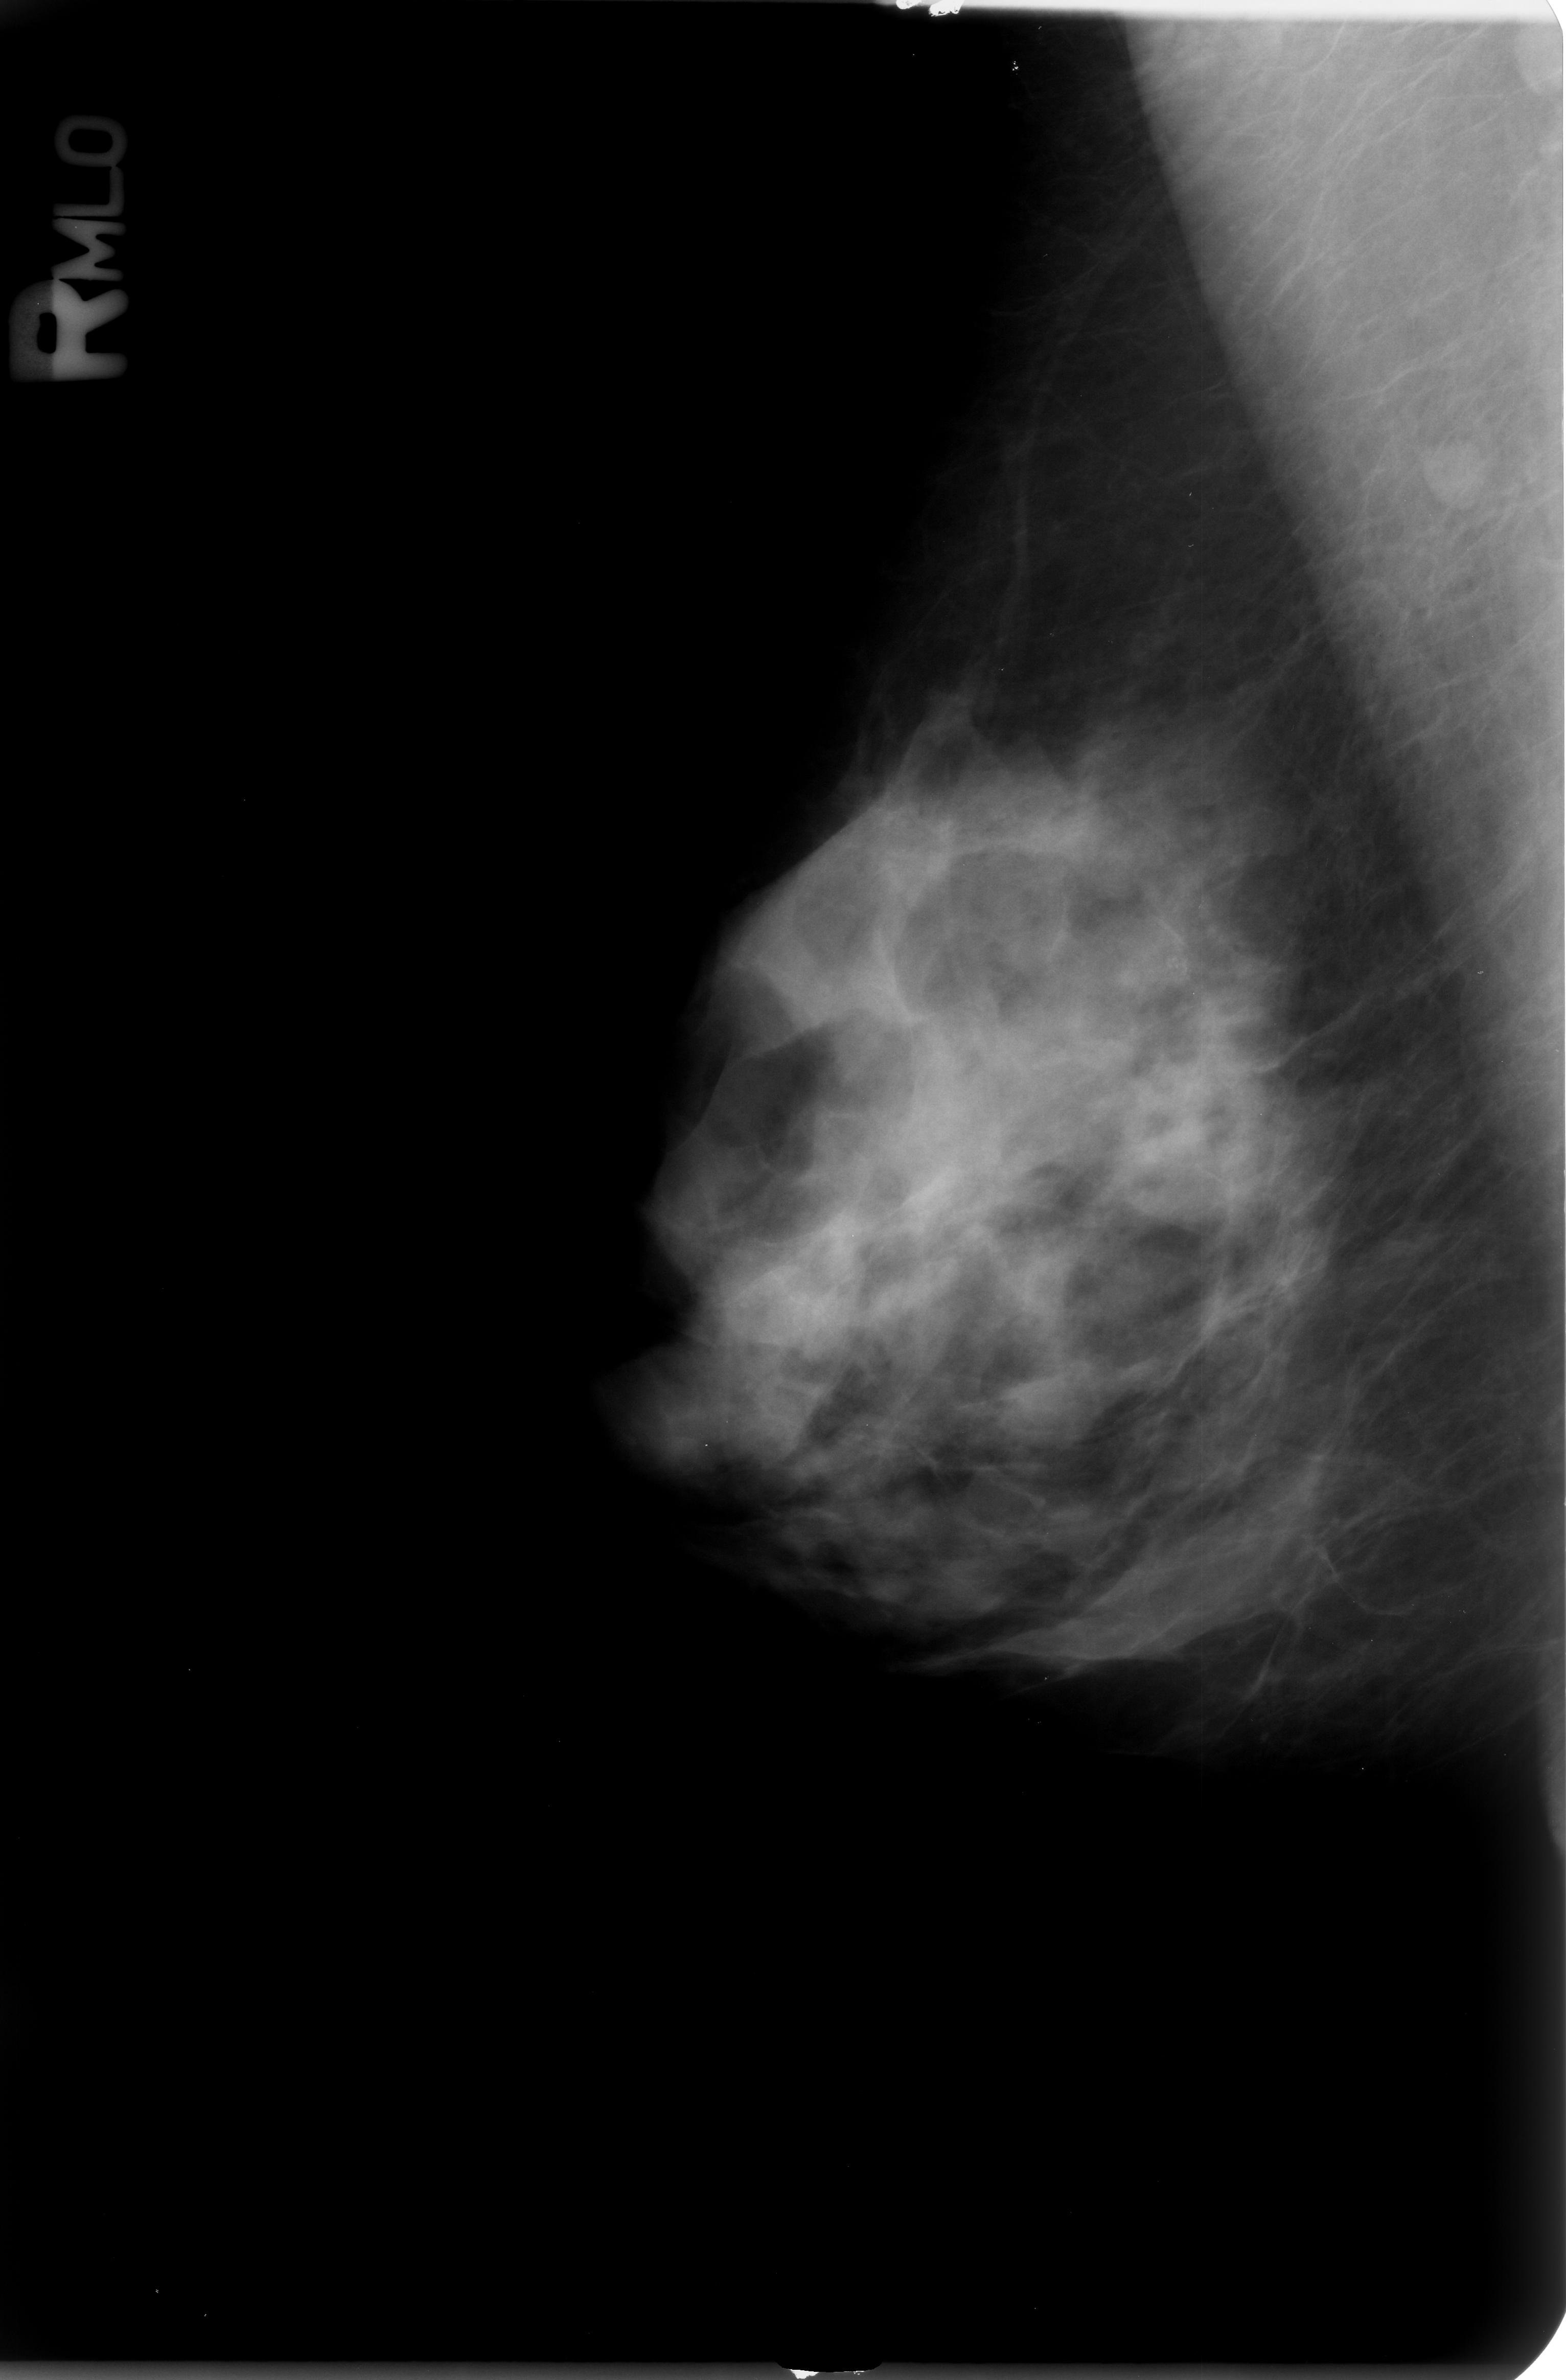
Digitized screen-film mammogram; right breast; mediolateral oblique (MLO) view; BI-RADS breast density category 3 (scale 1–4).
- Marked abnormality: calcifications, morphology amorphous, distribution clustered; BI-RADS assessment category 3; pathology result (as recorded, not read from the image): benign.